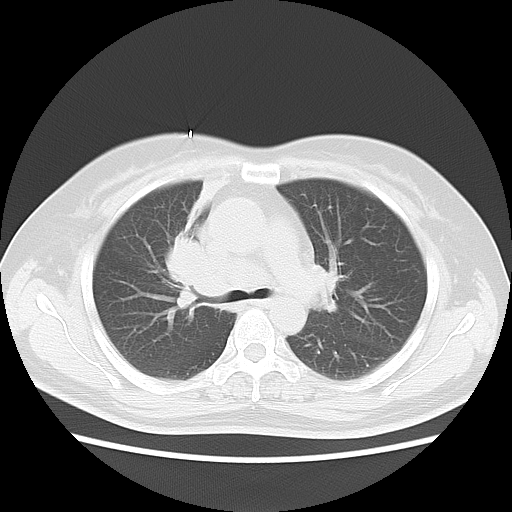
Chest CT, one axial slice; reconstruction kernel LUNG; lung window (W 1500 / L -600 HU); 5 mm slice thickness; 512 × 512 image matrix, field of view 350 × 350 mm. Female patient, age 54 years. From the clinical record (not read from this slice): clinical TNM (as recorded): T2 N3 M0; histopathological grade: G3.
Annotated regions visible in this slice (rectangle marked by the reading radiologist):
- lung tumour (recorded histology: small cell carcinoma): bounding box [x1, y1, x2, y2] px = [162, 235, 229, 323]